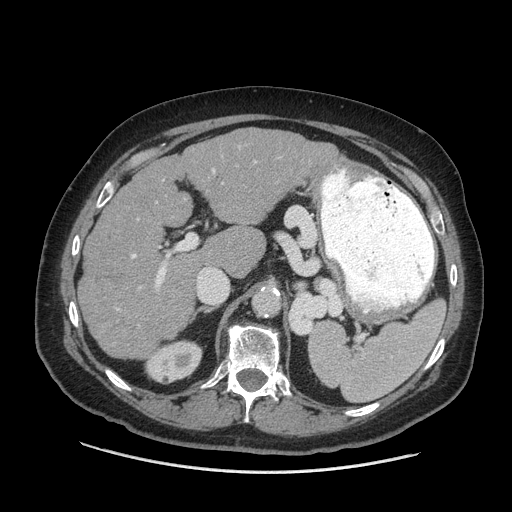
Contrast-enhanced abdominal CT (liver protocol), one axial slice; slice 38 of 77 in the series (ordered by position); reconstruction kernel STANDARD; soft-tissue window (W 400 / L 40 HU); 2.5 mm slice thickness; 512 × 512 image matrix, field of view 420 × 420 mm. Case-level facts recorded for this patient, not image findings: diagnosis: hepatocellular carcinoma (patient treated with transarterial chemoembolisation; whether this scan precedes or follows treatment is not stated here); TNM stage (as recorded): Stage-I; Child-Pugh class: A; tumour nodularity: uninodular; tumour size: 3.8 cm.
Structures marked on this image (semi-automatic segmentation, software-assisted and operator-edited):
- liver parenchyma outside the tumour (the mass and vessels are separate outlines, so this box may not span the whole liver): bounding box (x1, y1, x2, y2) in pixels: (78, 128, 340, 358)
- liver vessels: (117, 161, 256, 310)